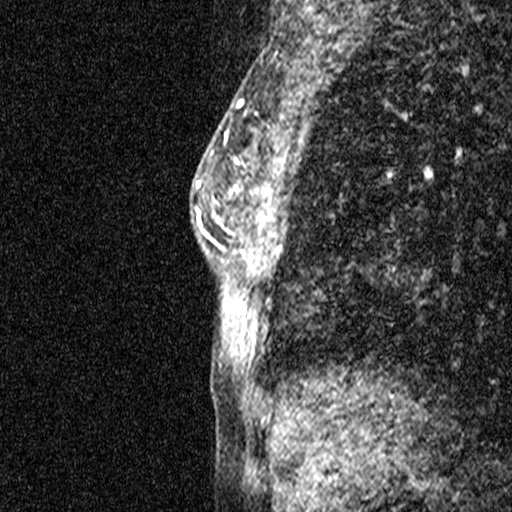
Breast MRI (dynamic contrast-enhanced), one sagittal slice; dynamic contrast-enhanced study with each time point stored as its own series, time point 2 of 3 at this slice position (early post-contrast, ordered by acquisition time); 1.5 T; TE 4.5 ms, TR 11 ms; 512 × 512 image matrix. Patient: female, 44 years. Case-level facts recorded for this patient, not image findings: setting: breast cancer imaged before/during neoadjuvant chemotherapy; receptor status: HR-positive, HER2-negative.
Annotated regions visible in this slice (semi-automatic segmentation, software-assisted and operator-edited):
- analysis volume of interest (the breast-tissue region the enhancement analysis was run in; not a lesion): bounding box (x1, y1, x2, y2) in pixels: (218, 118, 269, 291)
- tumour enhancement mask (voxels above the 90 % enhancement threshold inside the analysis volume of interest): (218, 132, 239, 222)